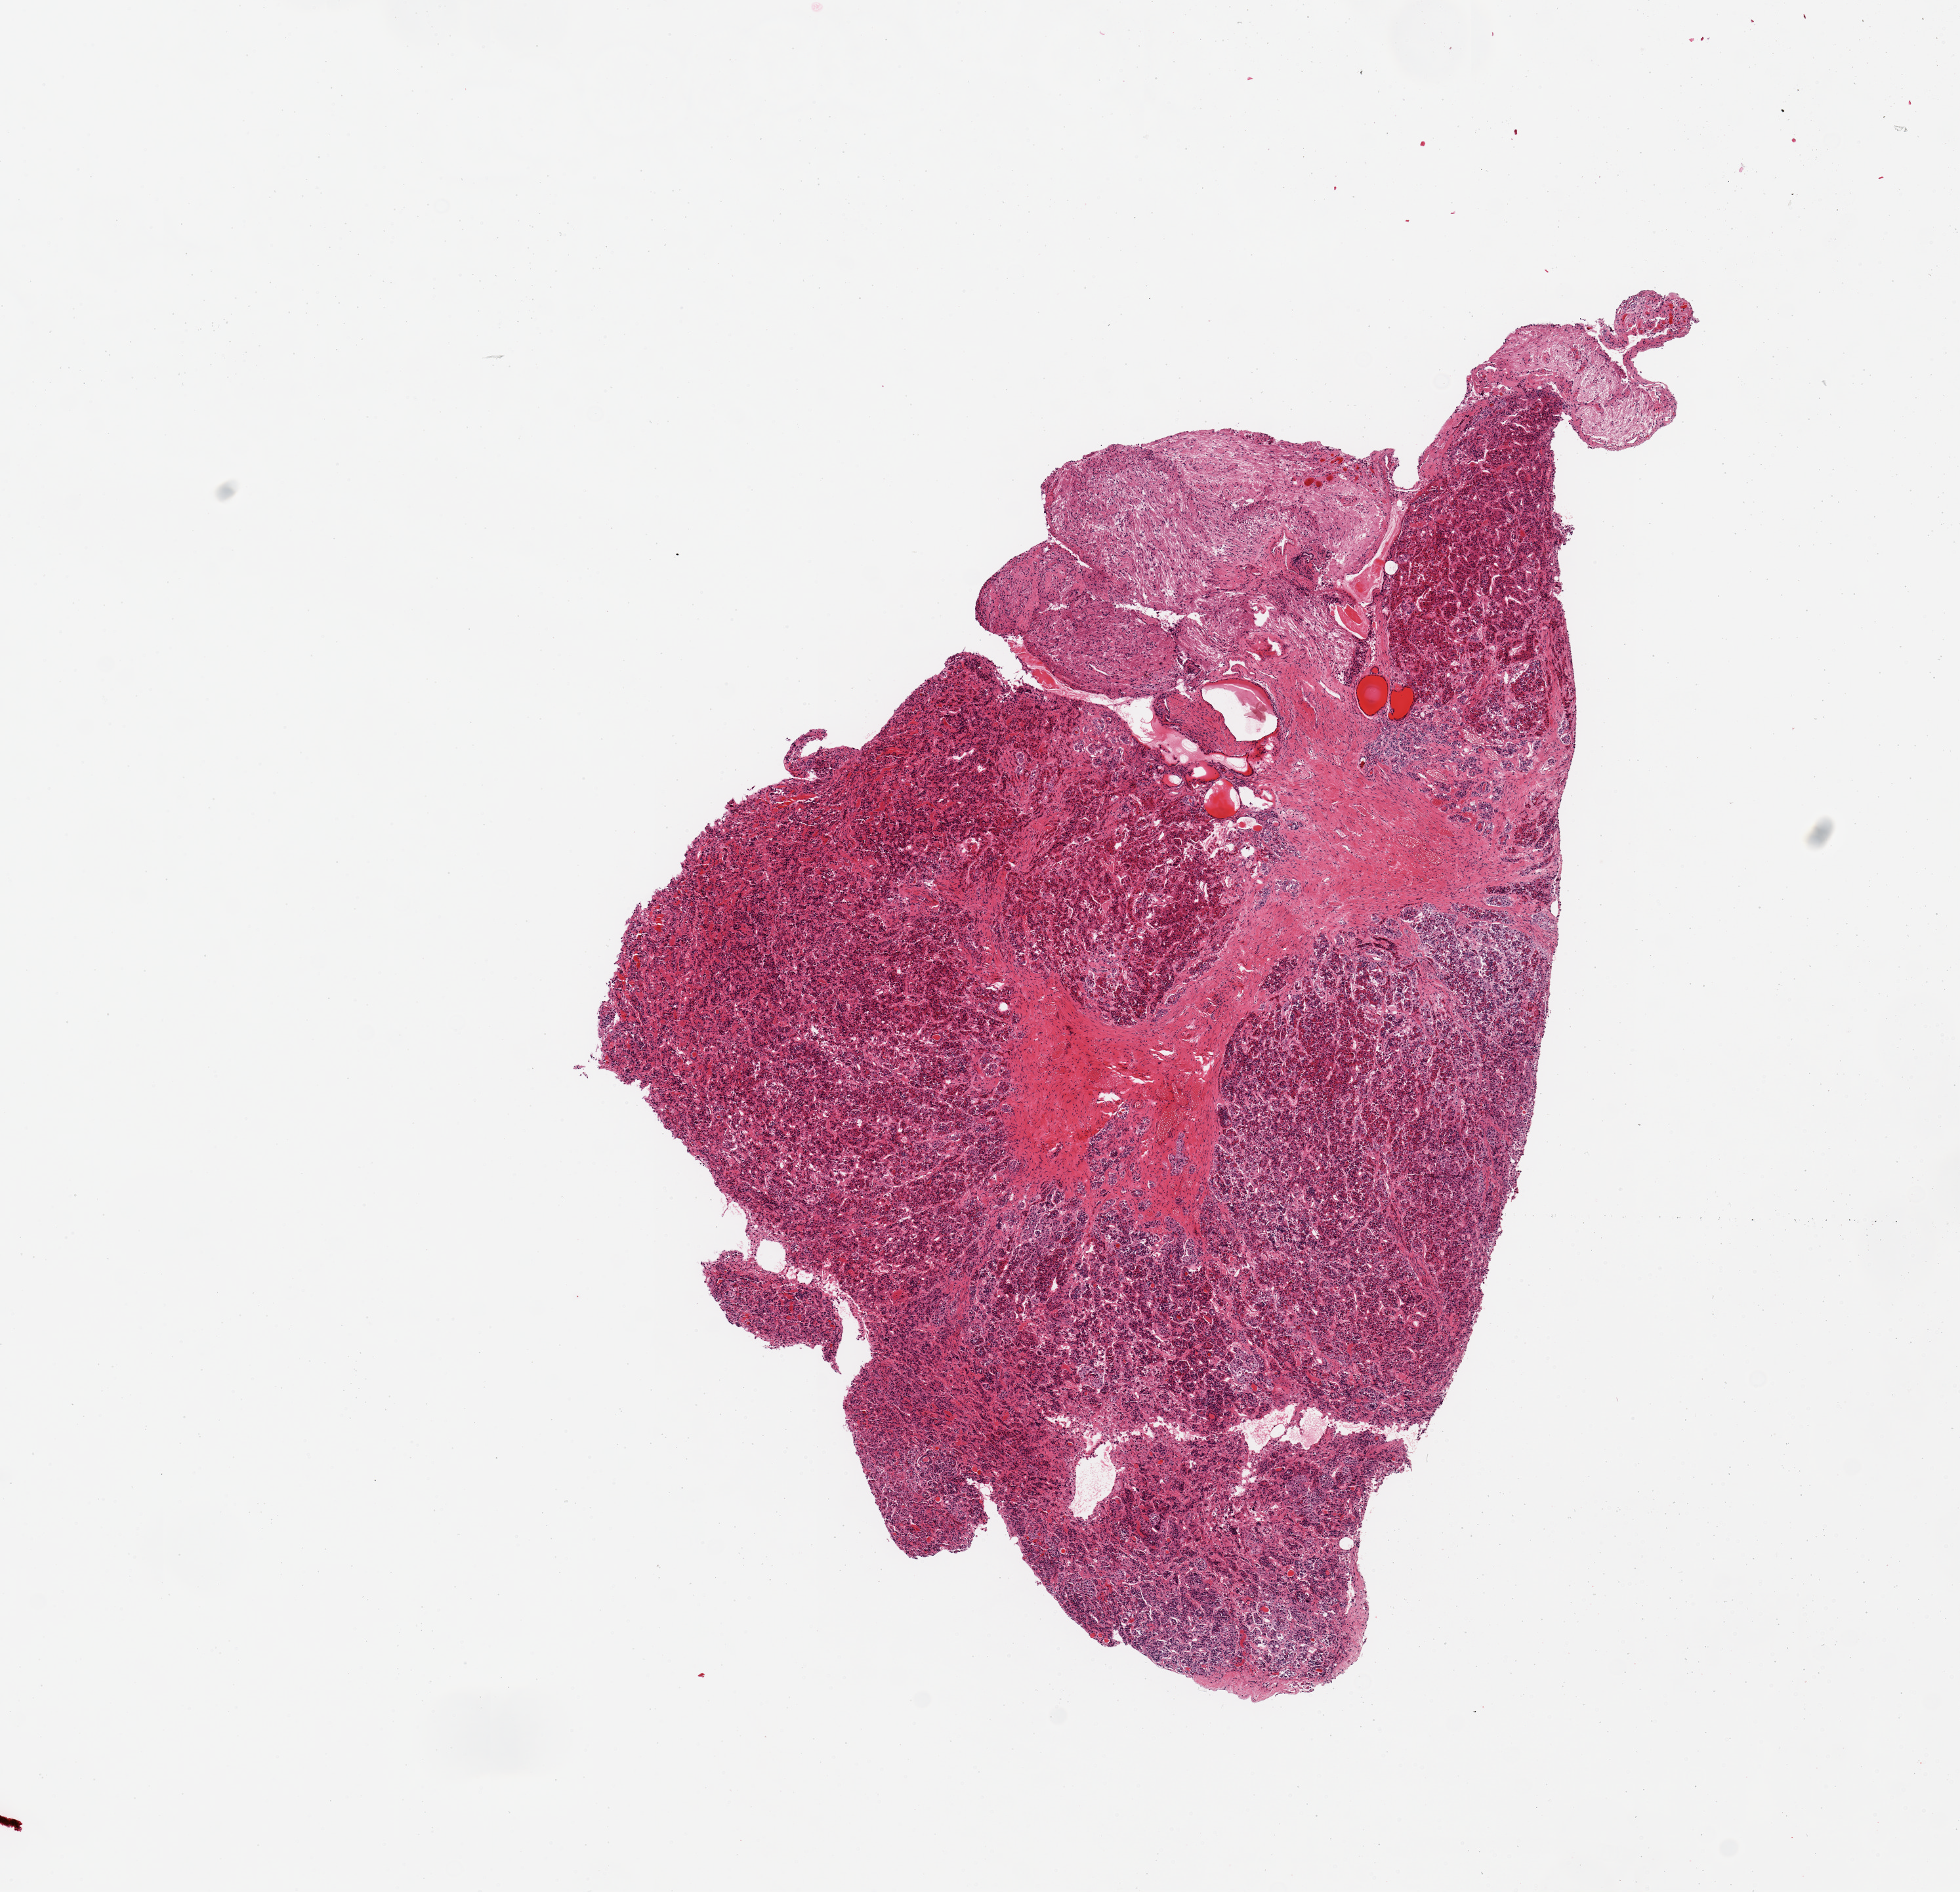
Digitized haematoxylin and eosin-stained section, low-resolution overview of the scanned area, about 11.8 x 11.4 mm. PAXgene-fixed paraffin-embedded (PFPE) section. Target tissue: pituitary. Tissue donor sample.
Pathologist's review note for this sample: 1 piece, mainly adenohypophysis; 2.5x1mm nubbin of neurohypophysis.